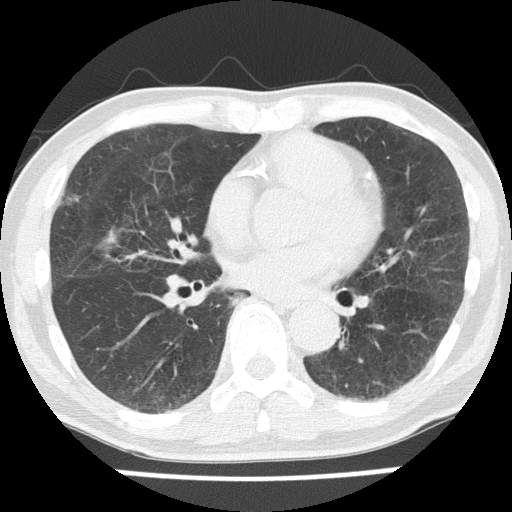
Axial slice from a low-dose chest CT screening exam, first (baseline) screen, lung window (W 1500 / L -600 HU), 2 mm slice thickness, lung (sharp) reconstruction kernel (FC51), slice 96 of 169 in the series. Male participant, aged 68 years at enrolment. Current smoker at enrolment.
- Expert reader's lesion annotation, bounding box (x1, y1, x2, y2) in pixels: (49, 184, 92, 217).
- No non-calcified nodule or mass ≥4 mm was recorded by the screening reader at this exam.
- Lung cancer was diagnosed 386 days after this screen: squamous cell carcinoma, NOS, right upper lobe, moderately differentiated (G2), stage IA (AJCC 6th edition), 10 mm at pathology.